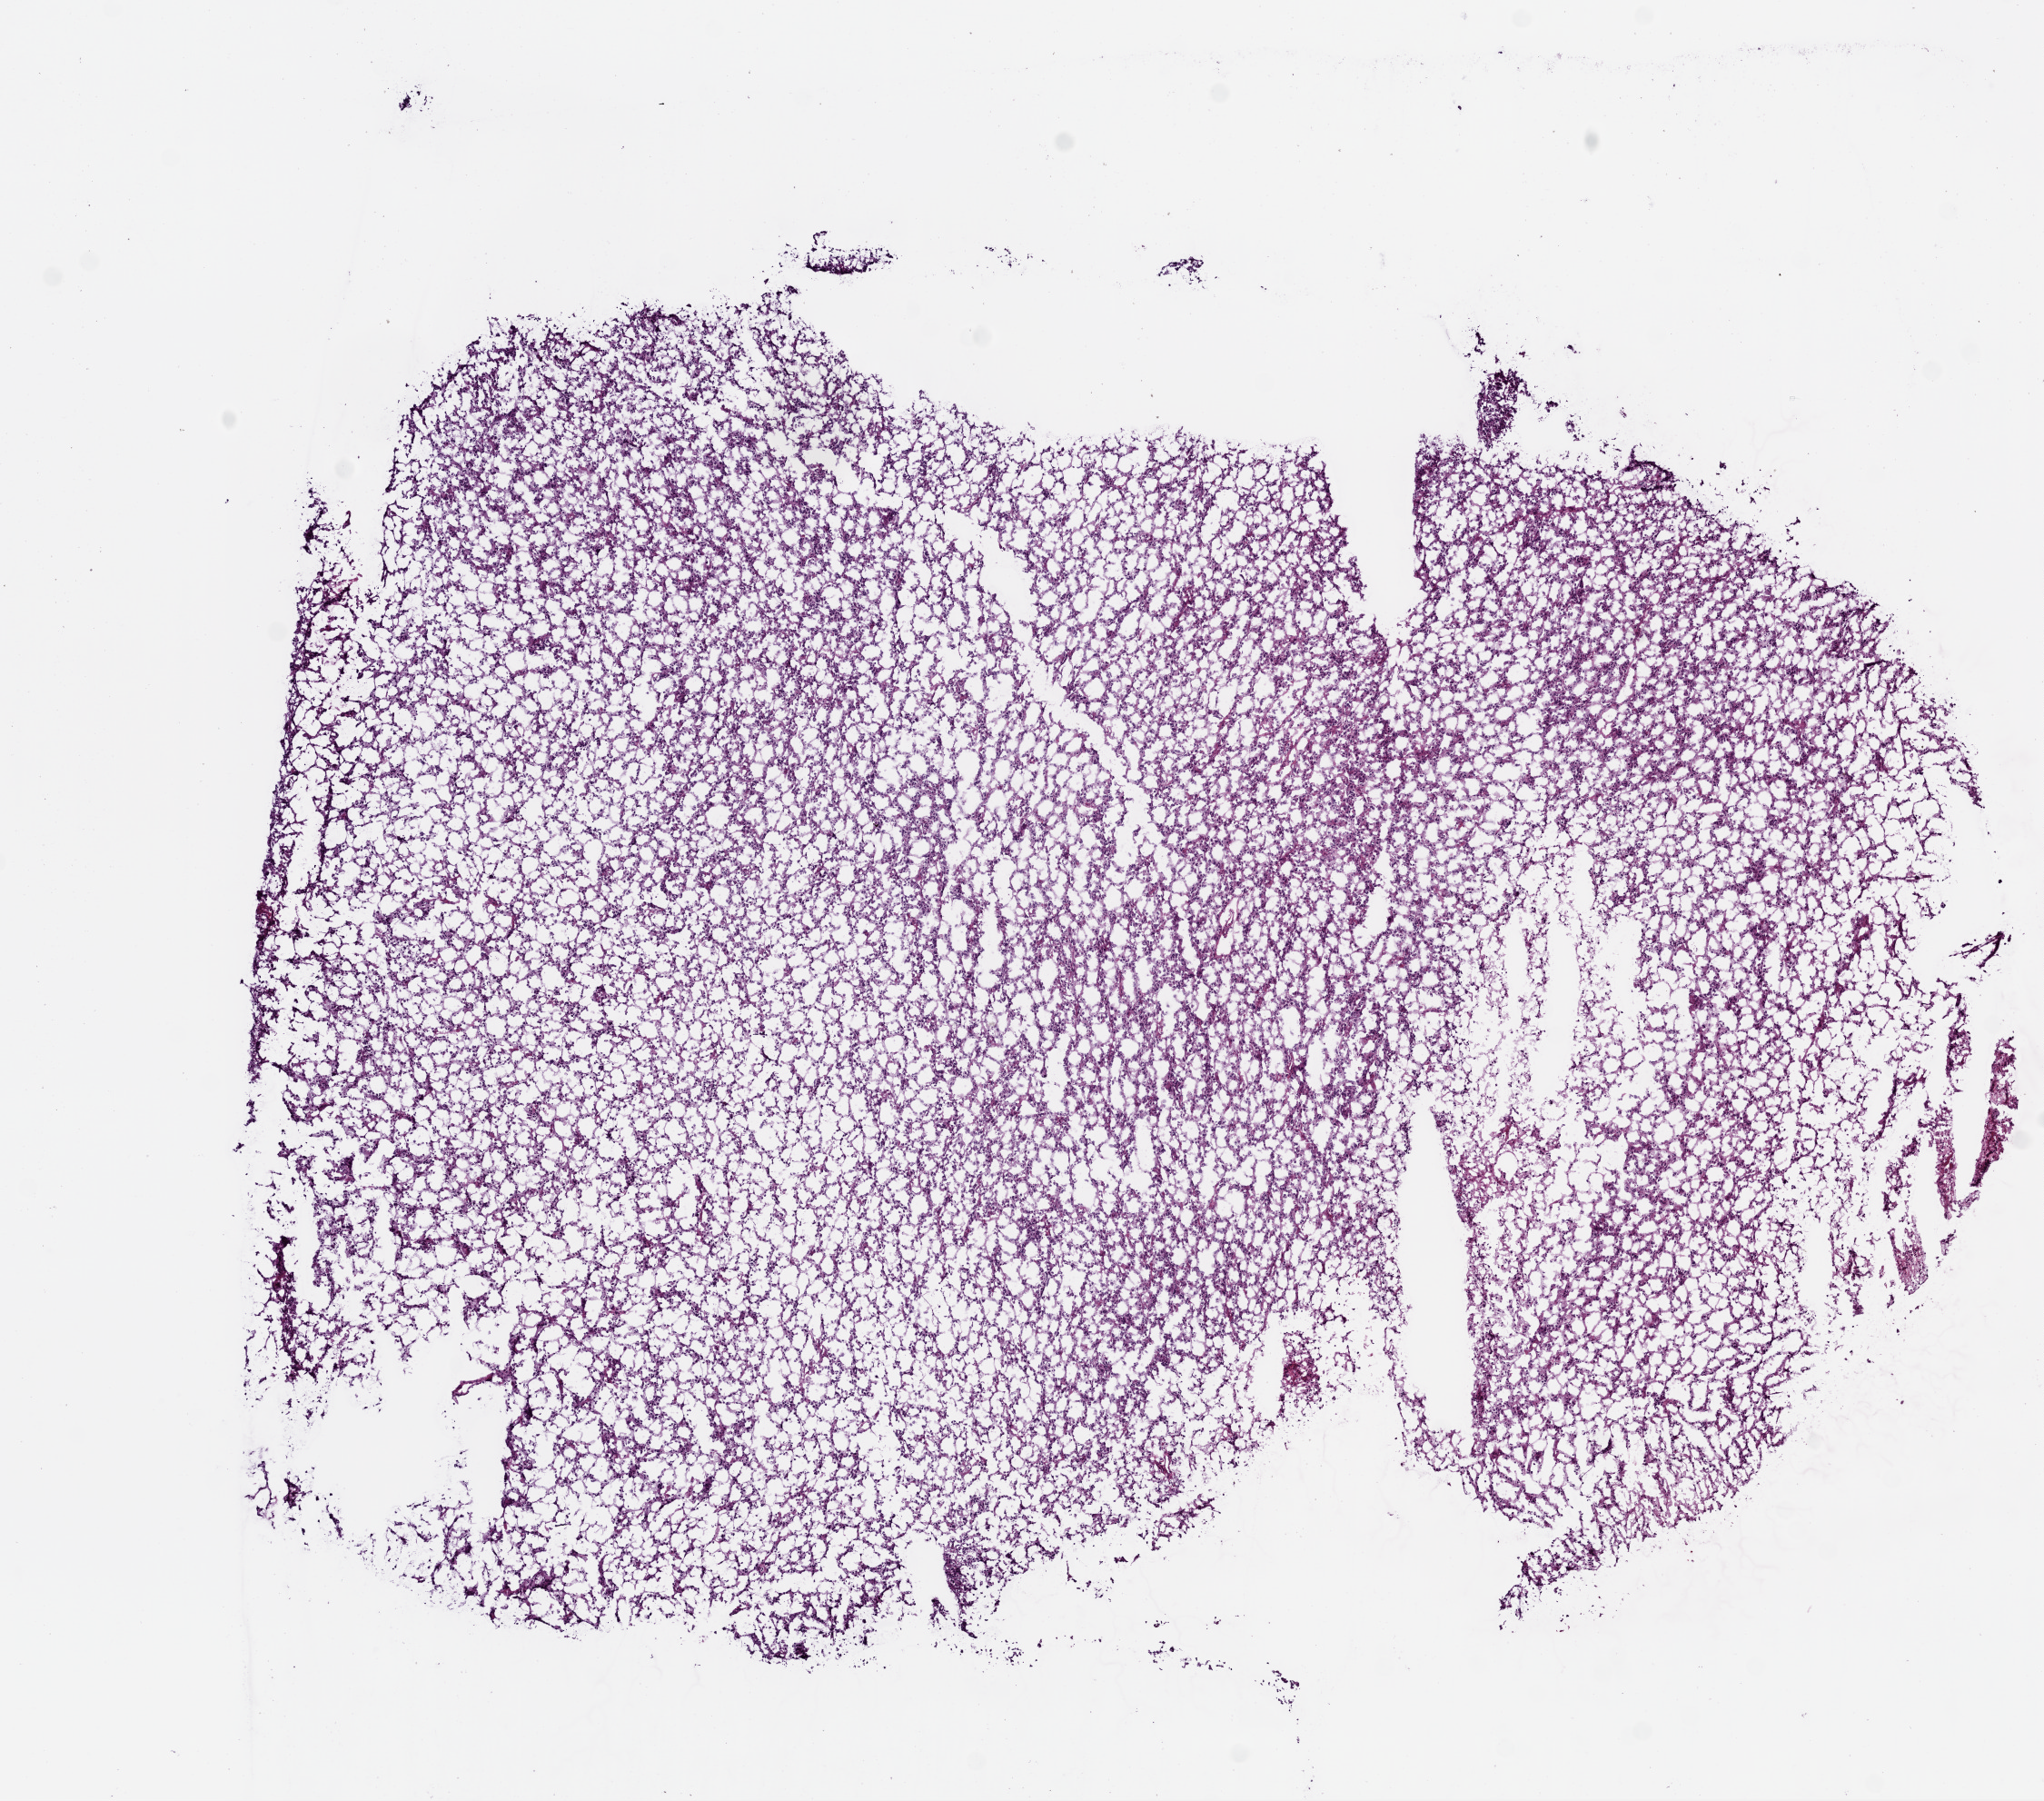
Hematoxylin and eosin (H&E) stained whole-slide image, a low-resolution overview of the entire scanned area, about 9.0 x 8.0 mm; frozen section; primary tumour sample from the brain. Patient: female, age at initial diagnosis 38 years. Histologic grade: G2 (moderately differentiated). Composition of this section per pathologist review: tumour cells 100%, tumour nuclei 75%, normal cells 0%, stromal cells 0%, necrosis 0%.
* diagnosis: Mixed glioma
* laterality: right